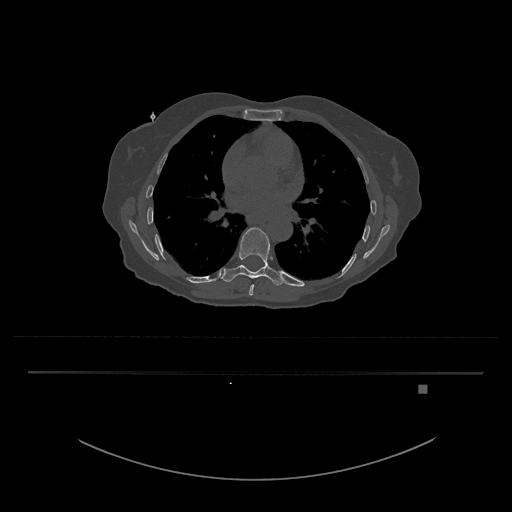
CT including the spine, one axial slice; slice 766 of 797 in the series (ordered by position); reconstruction kernel Br40s/3; 120 kVp; bone window (W 1800 / L 400 HU); 0.5 mm slice thickness; 512 × 512 image matrix, field of view 500 × 500 mm. Female patient, age 57 years. From the clinical record (not read from this slice): primary cancer: cervical.
Annotated regions visible in this slice (semi-automatic segmentation, software-assisted and operator-edited):
- T8 vertebra: box from (x=249, y=284) to (x=255, y=296) px
- T9 vertebra: (x=221, y=227)–(x=286, y=286)